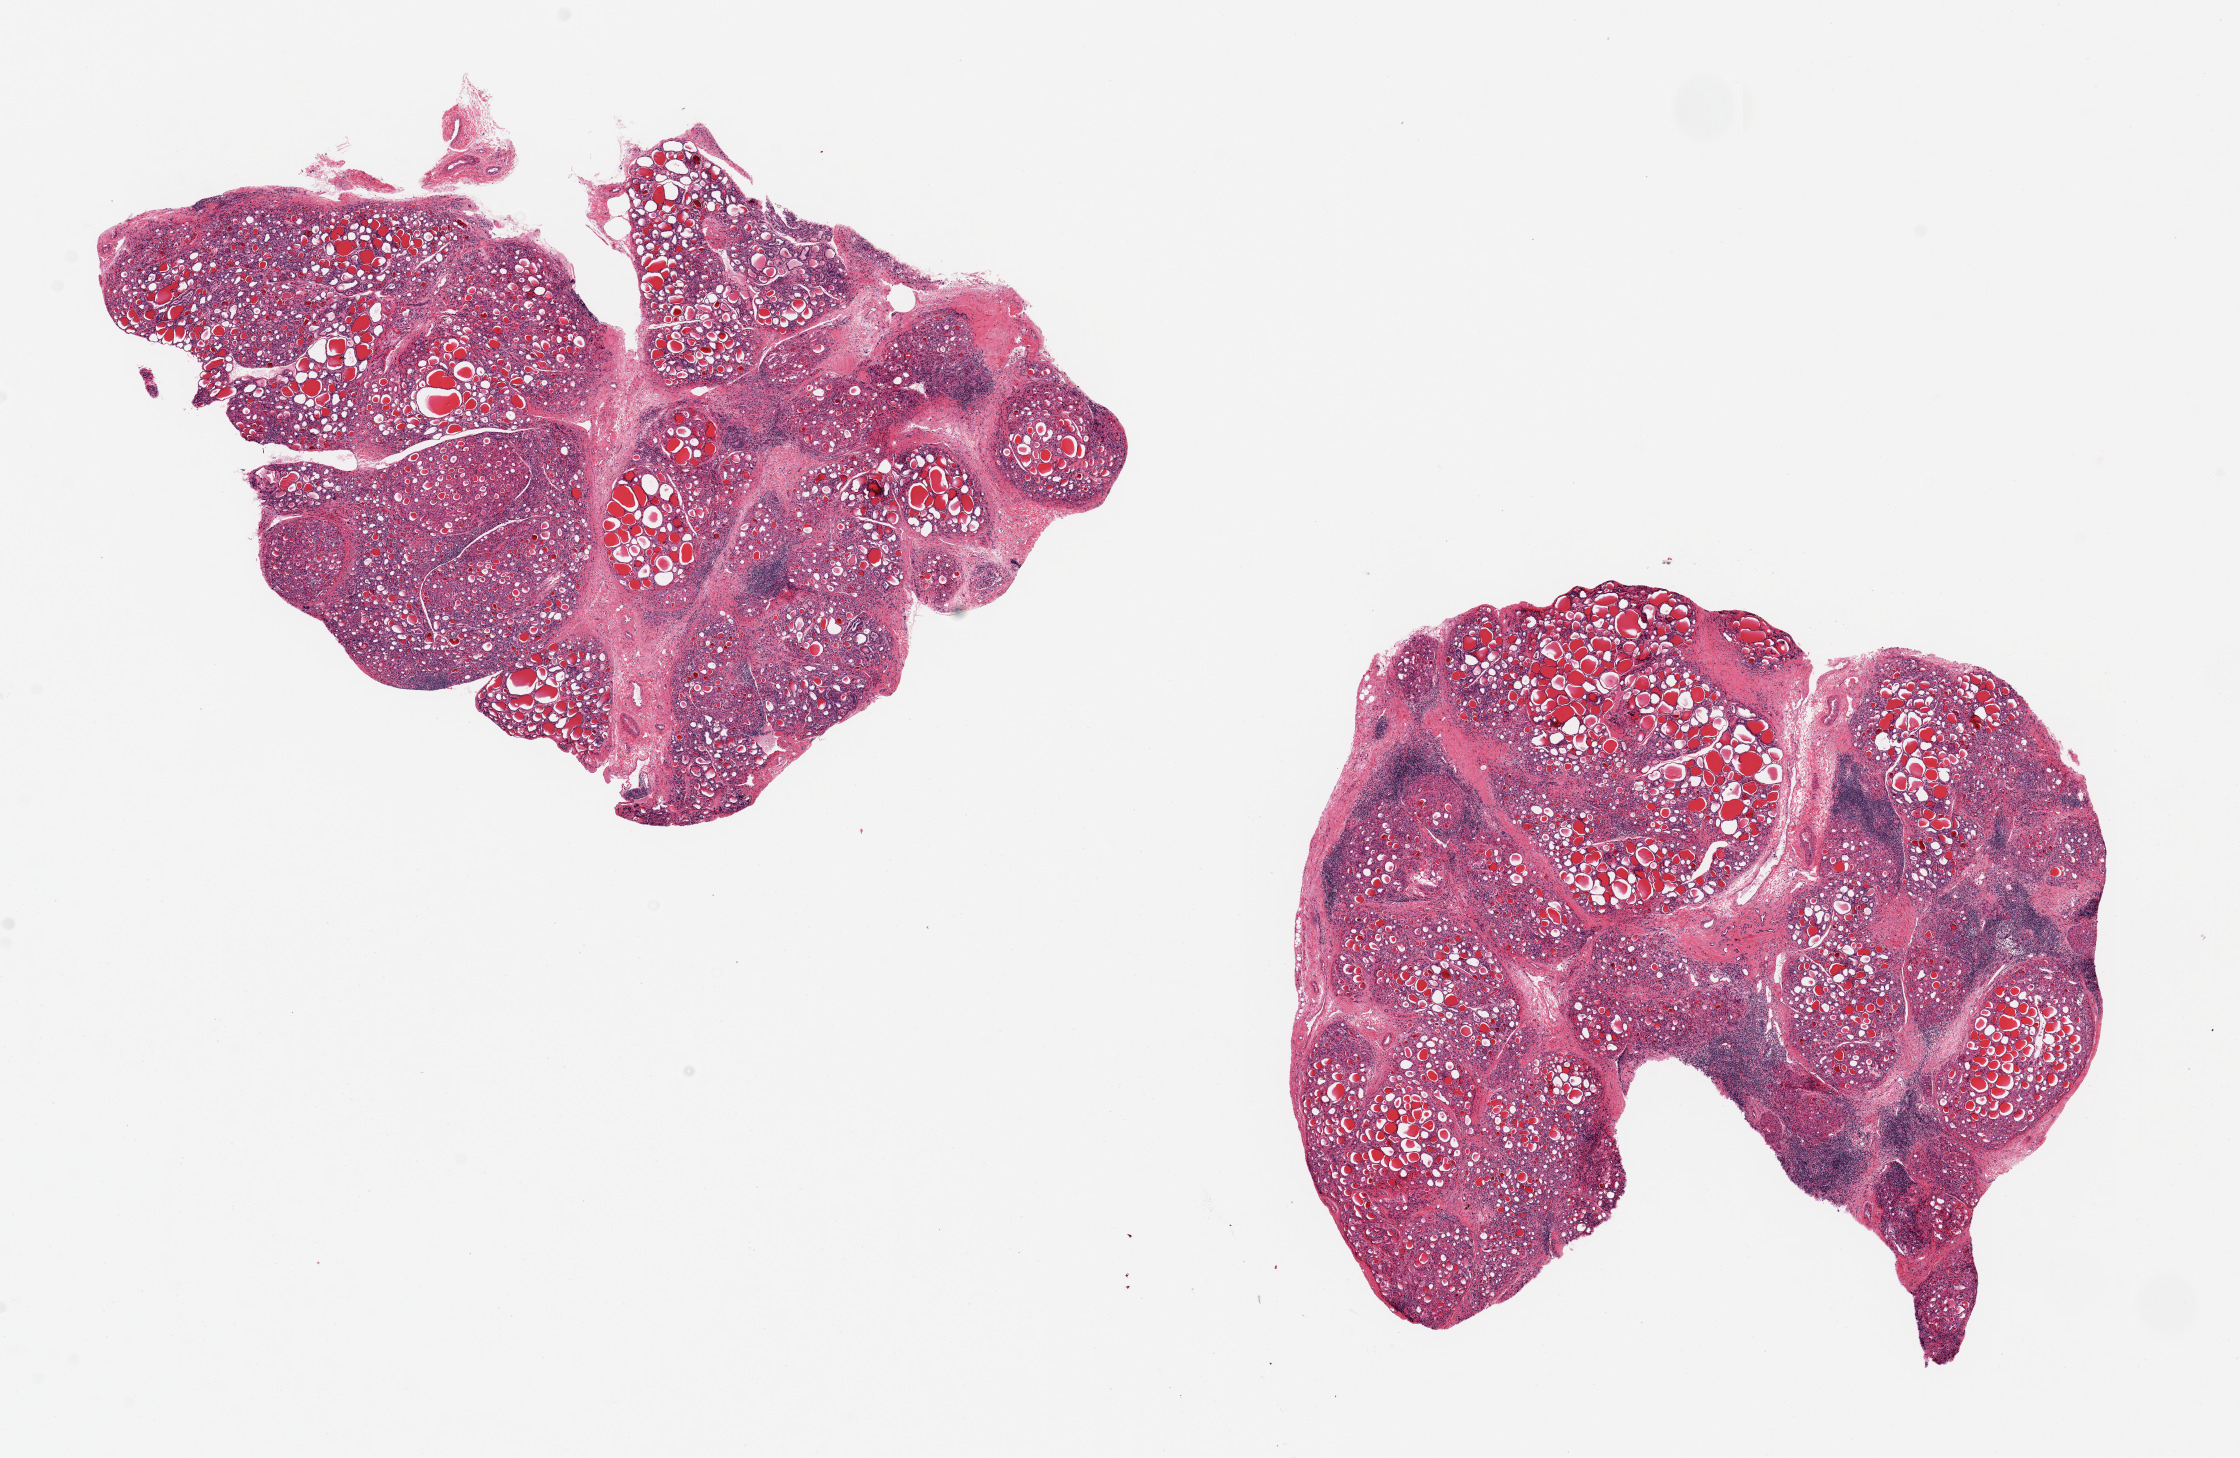
Haematoxylin and eosin whole-slide image — shown as a low-resolution overview of the whole scanned area (about 17.7 x 11.5 mm); PAXgene-fixed paraffin-embedded (PFPE) section; target tissue: thyroid; tissue donor sample. Female donor.
Pathologist's review note for this sample: 2 aliquots, ~7x6mm, diffuse lymphocytic/Hashimoto's thyroiditis with prominent regressive changes.